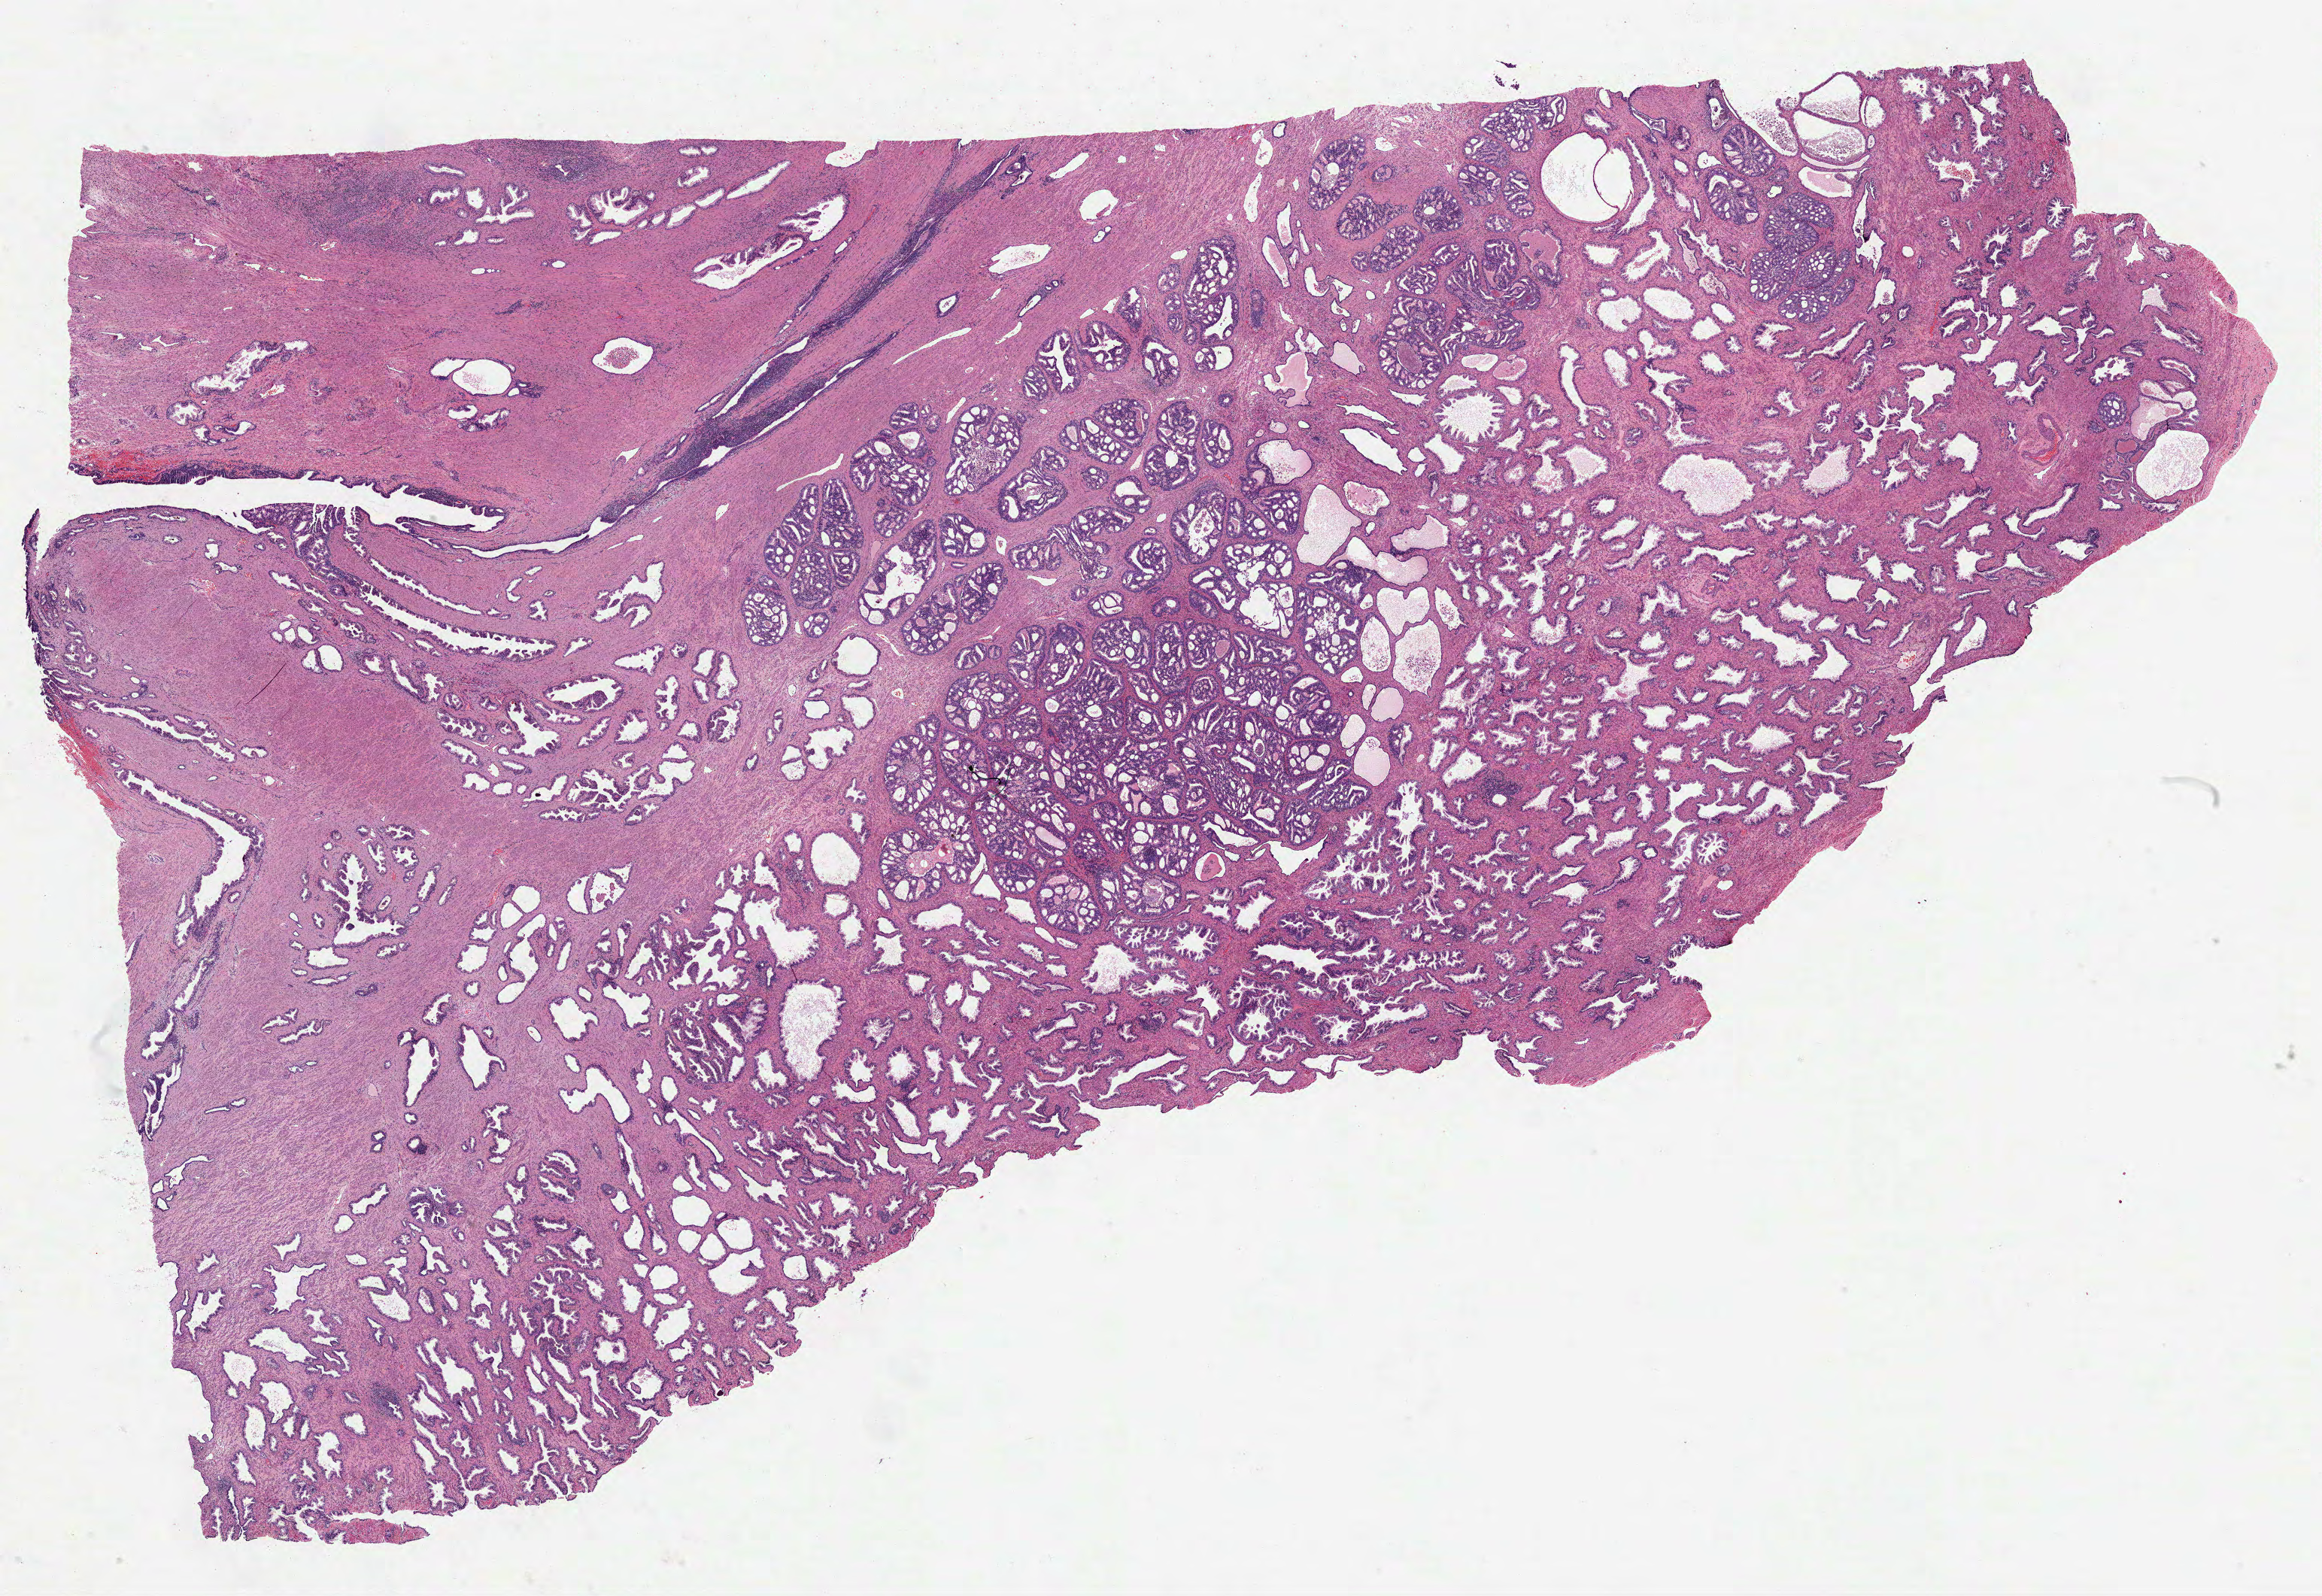
Whole-slide histology image, H&E — shown as a low-resolution overview of the whole scanned area (about 24.9 x 17.1 mm). Formalin-fixed paraffin-embedded (FFPE) diagnostic section. Primary tumour sample from the prostate. Male, age 71 years at initial diagnosis. Gleason score: 8 (4+4).
- histologic diagnosis: Acinar cell carcinoma (prostate gland)